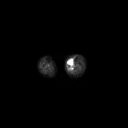
FDG PET of an extremity soft-tissue mass (from a PET/CT study), one axial slice. Position 131 of 223 along the scan axis. 3.27 mm slice thickness. 128 × 128 image matrix, field of view 700 × 700 mm. Female patient, age 70 years. Case-level facts recorded for this patient, not image findings: histological type: extraskeletal high grade osteogenic sarcoma; grade: high; site of the primary tumour: left calf.
Annotated regions visible in this slice (expert contour drawn on MRI and transferred to this co-registered scan by the dataset authors):
- gross tumour volume (mass): box from (x=68, y=62) to (x=73, y=68) px